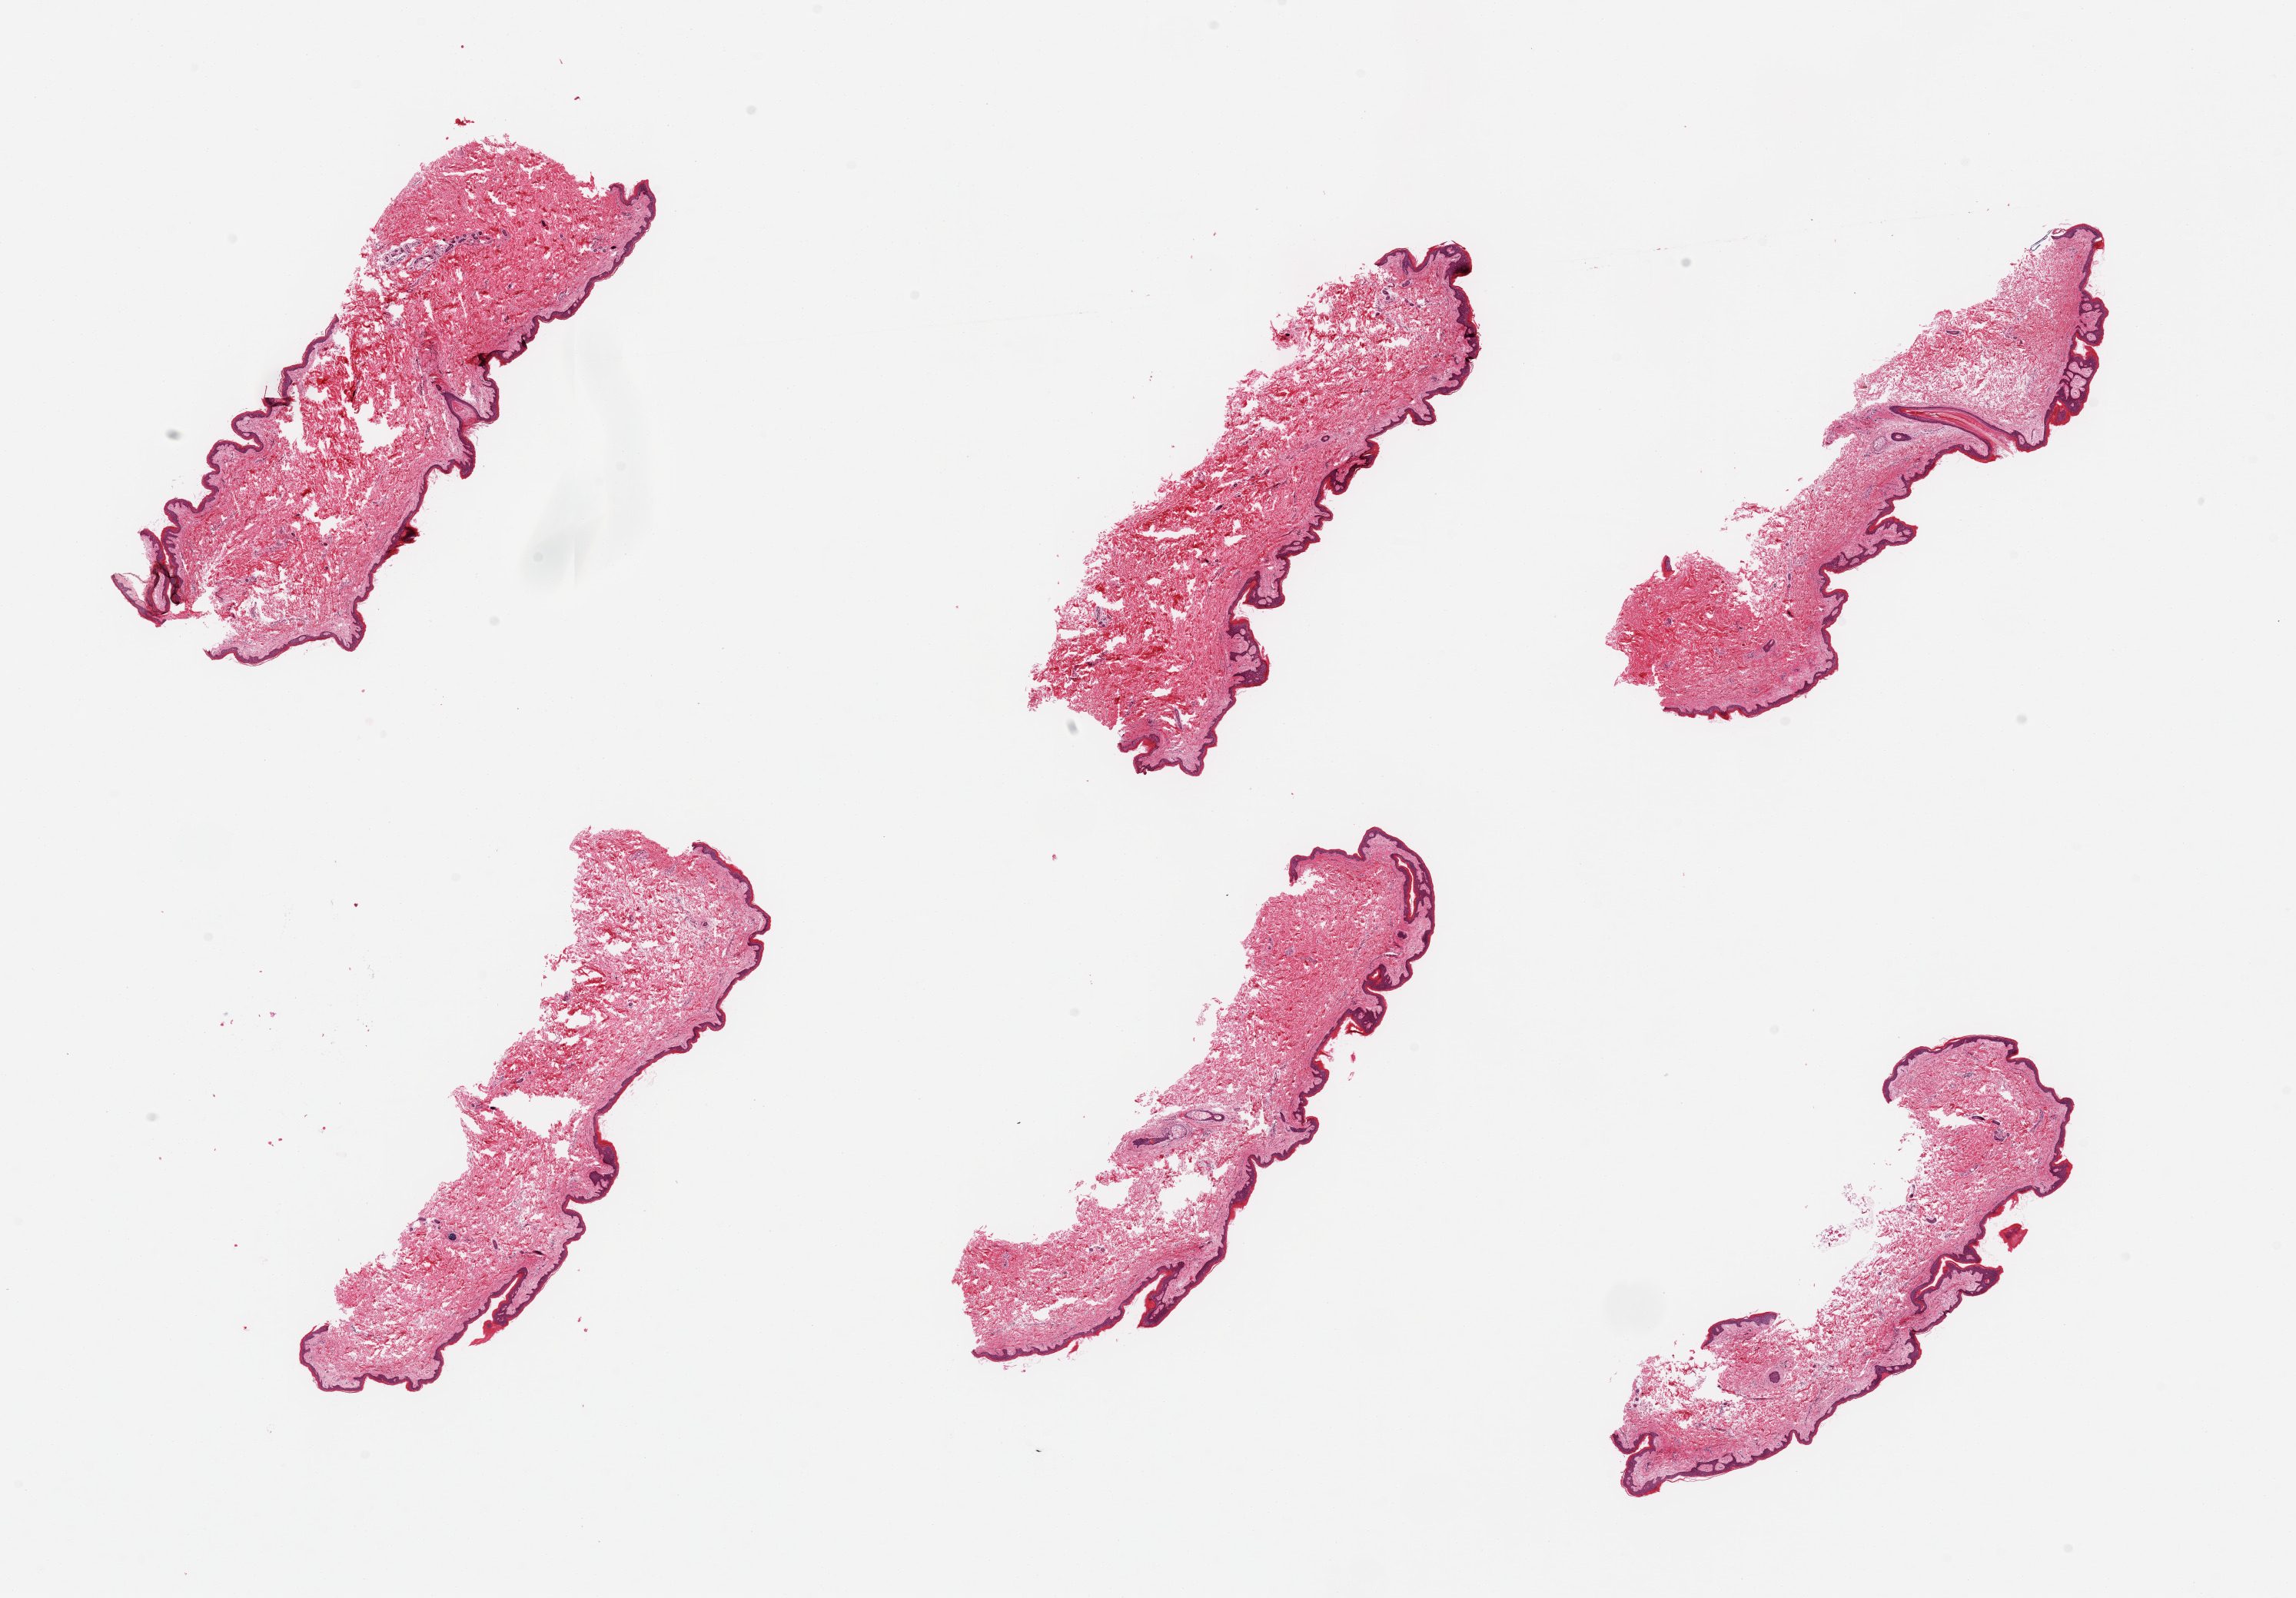
Digitized hematoxylin and eosin (H&E)-stained section — whole scanned area (about 23.6 x 16.4 mm) shown as a low-resolution overview, PAXgene-fixed paraffin-embedded (PFPE) section, sampled site (target tissue): skin of suprapubic region, donor tissue sample. Donor: male.
Pathologist's review note for this sample: 6 pieces; essentially well trimmed with numerous empty spaces likely fixation problem.